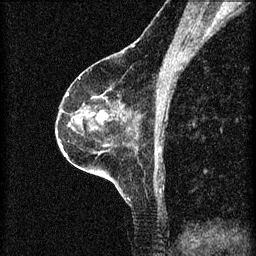
Breast MRI (dynamic contrast-enhanced), one sagittal slice; position 38 of 60 along the scan axis; 3 images stored at this slice position (order not interpretable as contrast timing); 1.5 T; TE 4.2 ms, TR 8.2 ms; 2 mm slice thickness; 256 × 256 image matrix, field of view 180 × 180 mm. Female patient, age 60 years.
Structures marked on this image (semi-automatically segmented with operator editing):
- analysis volume of interest (the breast-tissue region the enhancement analysis was run in; not a lesion): bounding box [x1, y1, x2, y2] px = [78, 96, 114, 131]
- tumour enhancement mask (voxels above the 70 % enhancement threshold inside the analysis volume of interest): [93, 96, 107, 119]